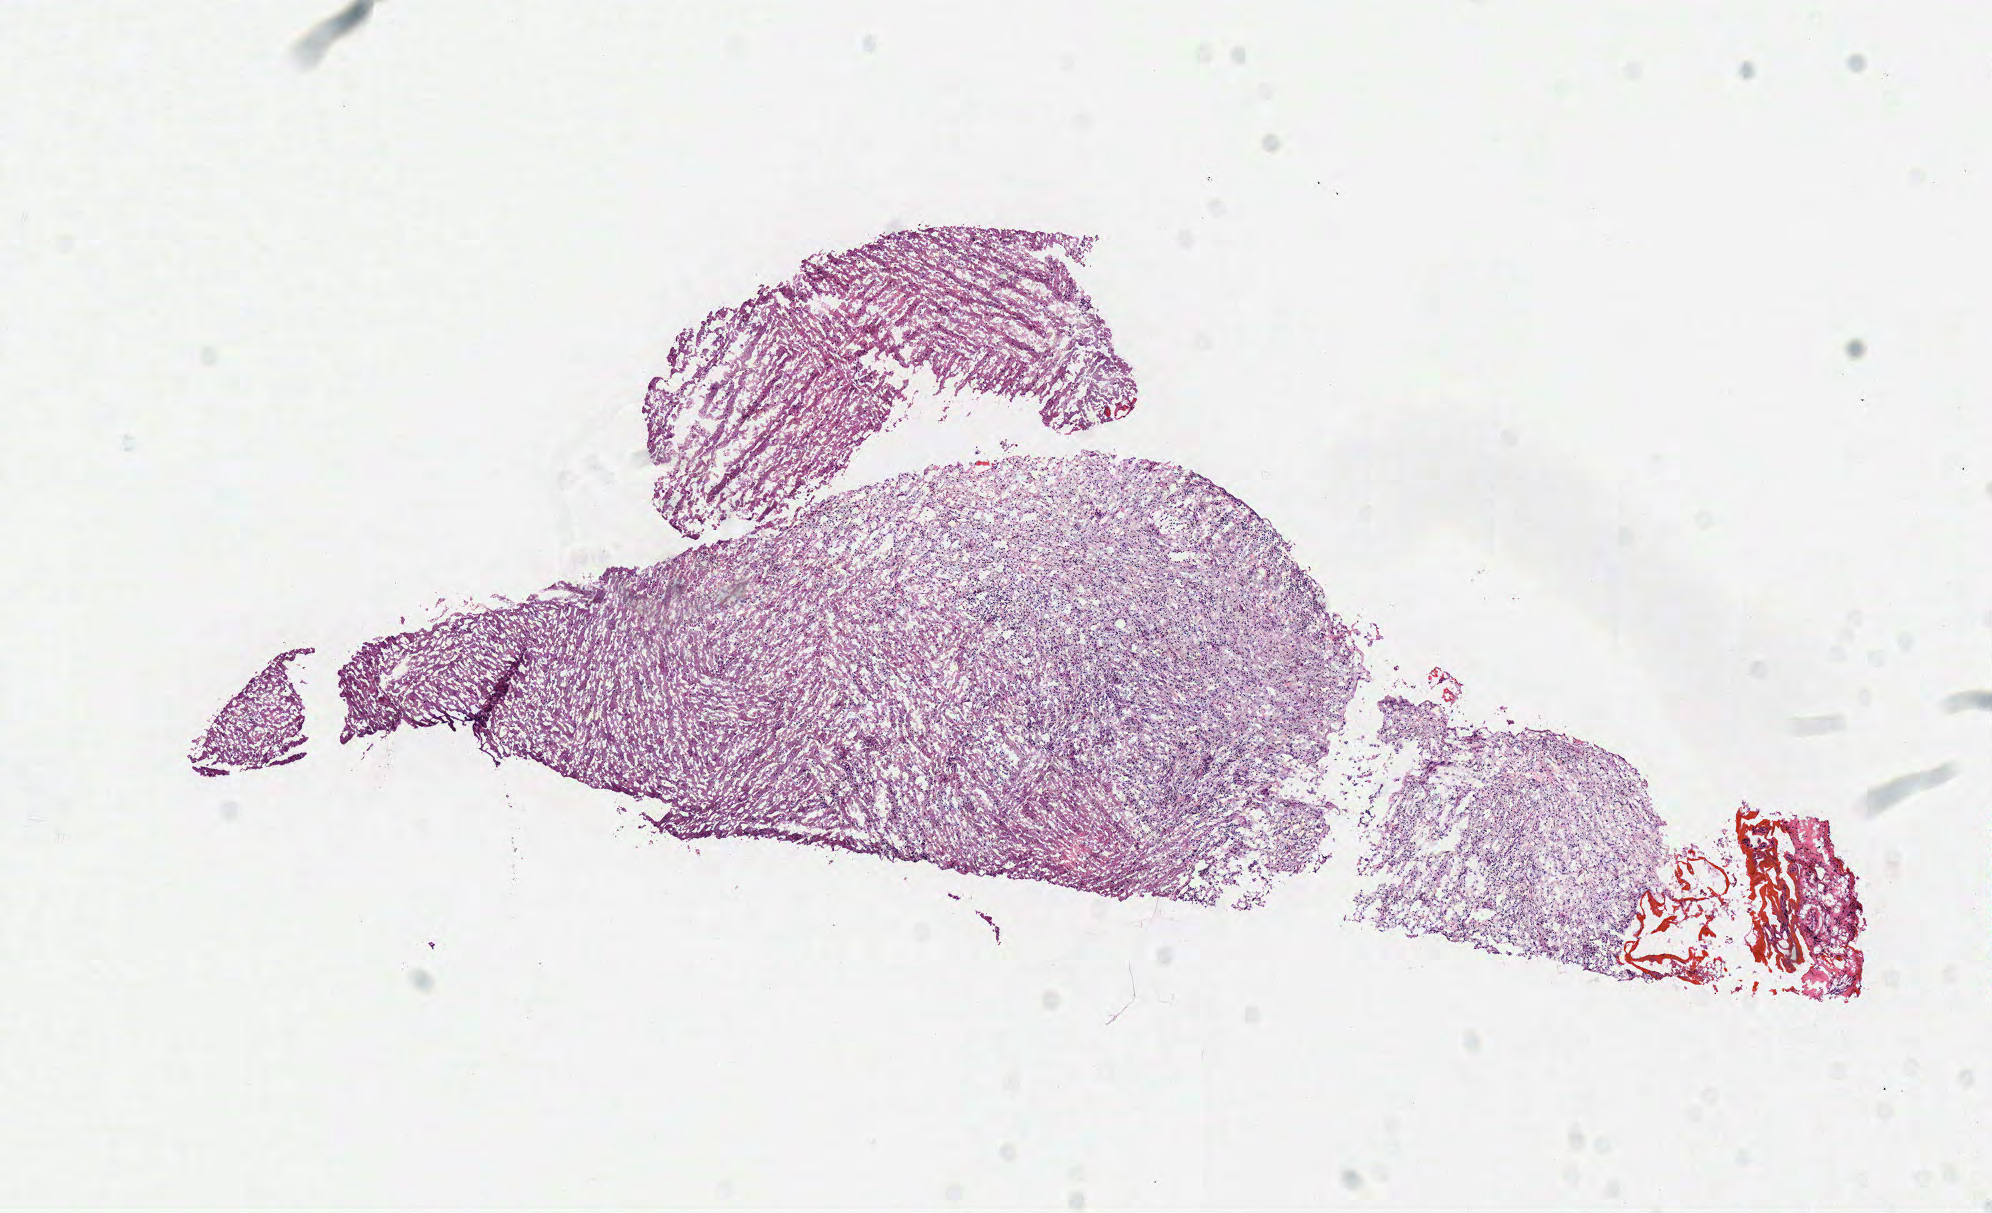
Whole-slide histology image, Hematoxylin and eosin (H&E) stained, whole scanned area (about 7.8 x 4.8 mm, slide scanned at 40x) shown as a low-resolution overview; frozen section from the top of the tissue portion; primary tumour sample from the brain. Male patient; age at initial diagnosis 23 years. Histologic grade: G3 (poorly differentiated). Slide review estimates, as recorded: tumour cells 100%, tumour nuclei 70%, normal cells 0%, stromal cells 0%, necrosis 0%.
* pathologic diagnosis: Astrocytoma, anaplastic
* laterality: right